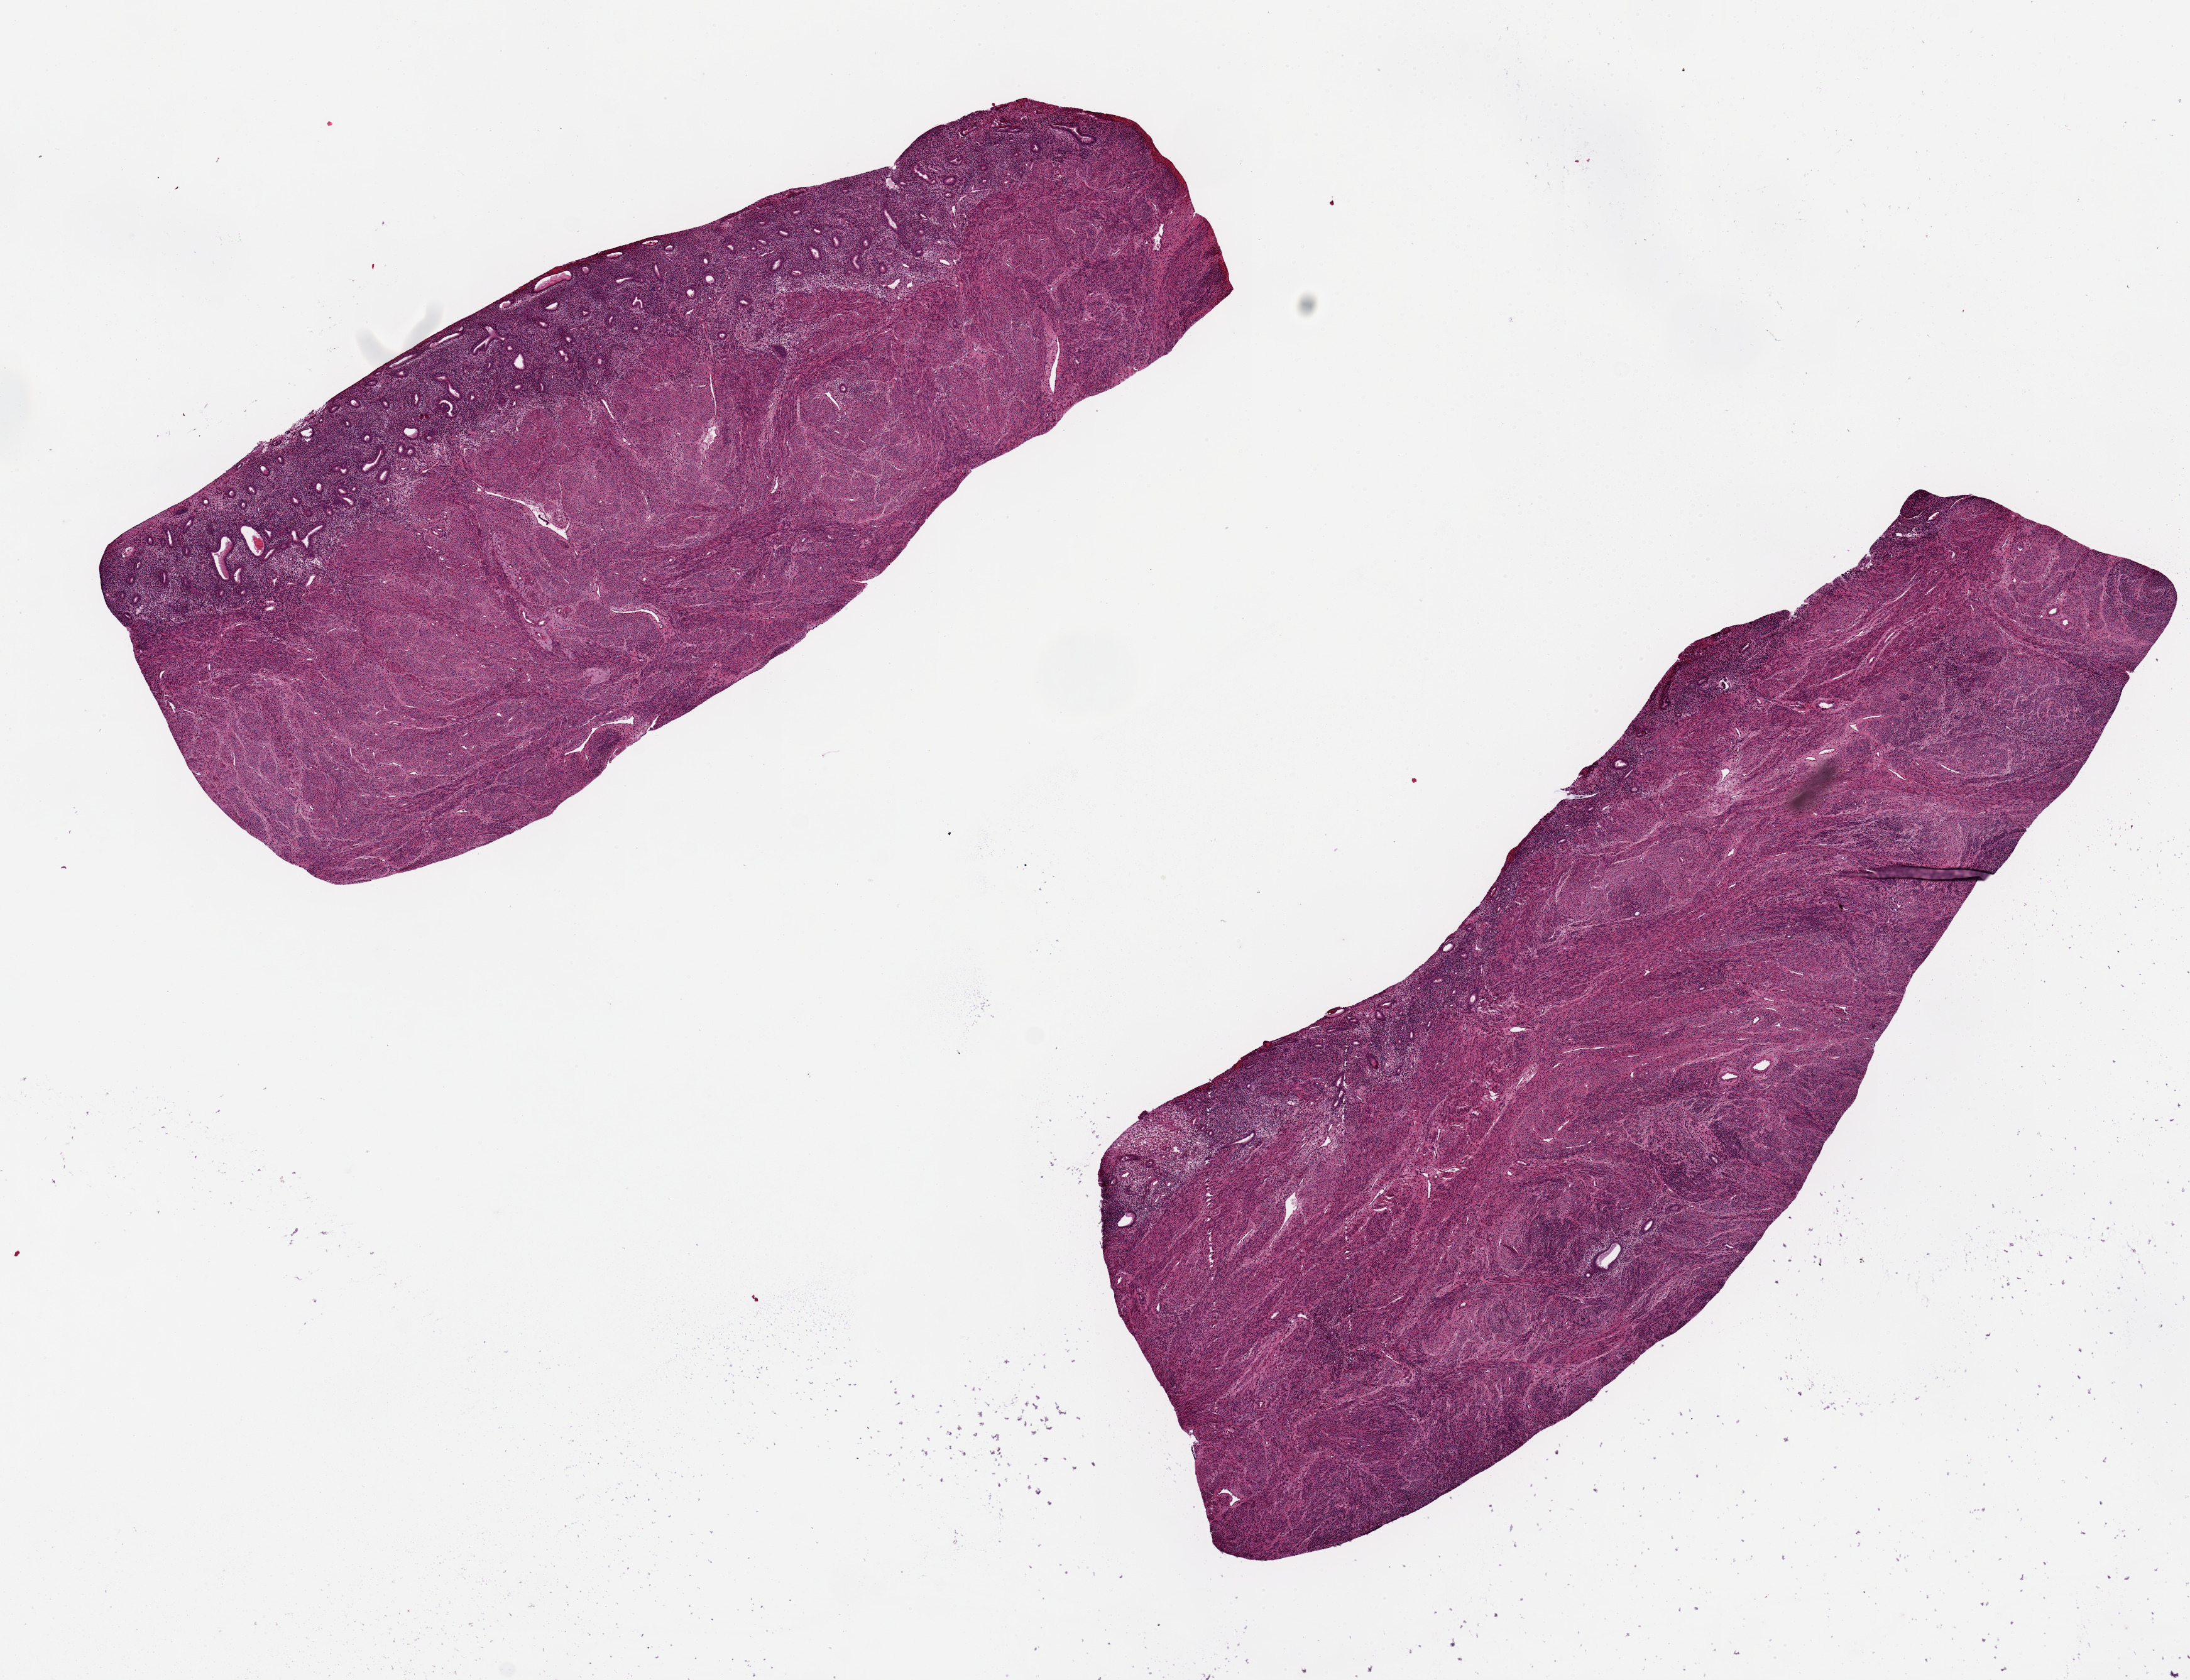
Whole-slide image, hematoxylin and eosin (H&E) stain, shown as a low-resolution overview of the whole scanned area (about 13.8 x 10.6 mm), PAXgene-fixed paraffin-embedded (PFPE) section, target tissue: uterus, tissue donor sample. Female donor.
• reviewer comment on this tissue sample: 2 pieces up to ~8x3mm, atrophic endometrium